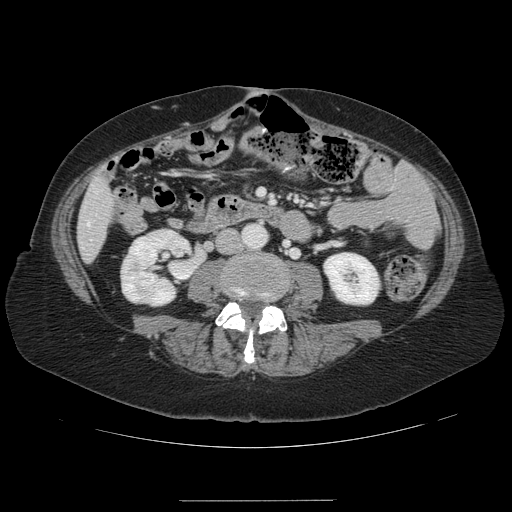
Contrast-enhanced abdominal CT, one axial slice. Position 21 of 141 along the scan axis. 120 kVp. Intravenous contrast given. Soft-tissue window (W 400 / L 40 HU). 2.5 mm slice thickness. 512 × 512 image matrix, field of view 393 × 393 mm. Female patient, age 74 years. From the clinical record (not read from this slice): diagnosis: colorectal cancer liver metastases, imaged before liver resection; multiple liver metastases: yes.
Structures marked on this image (expert manual segmentation):
- liver: box from (x=78, y=181) to (x=114, y=261) px
- planned liver remnant (the part of the liver to remain after resection): (x=80, y=198)–(x=111, y=251)